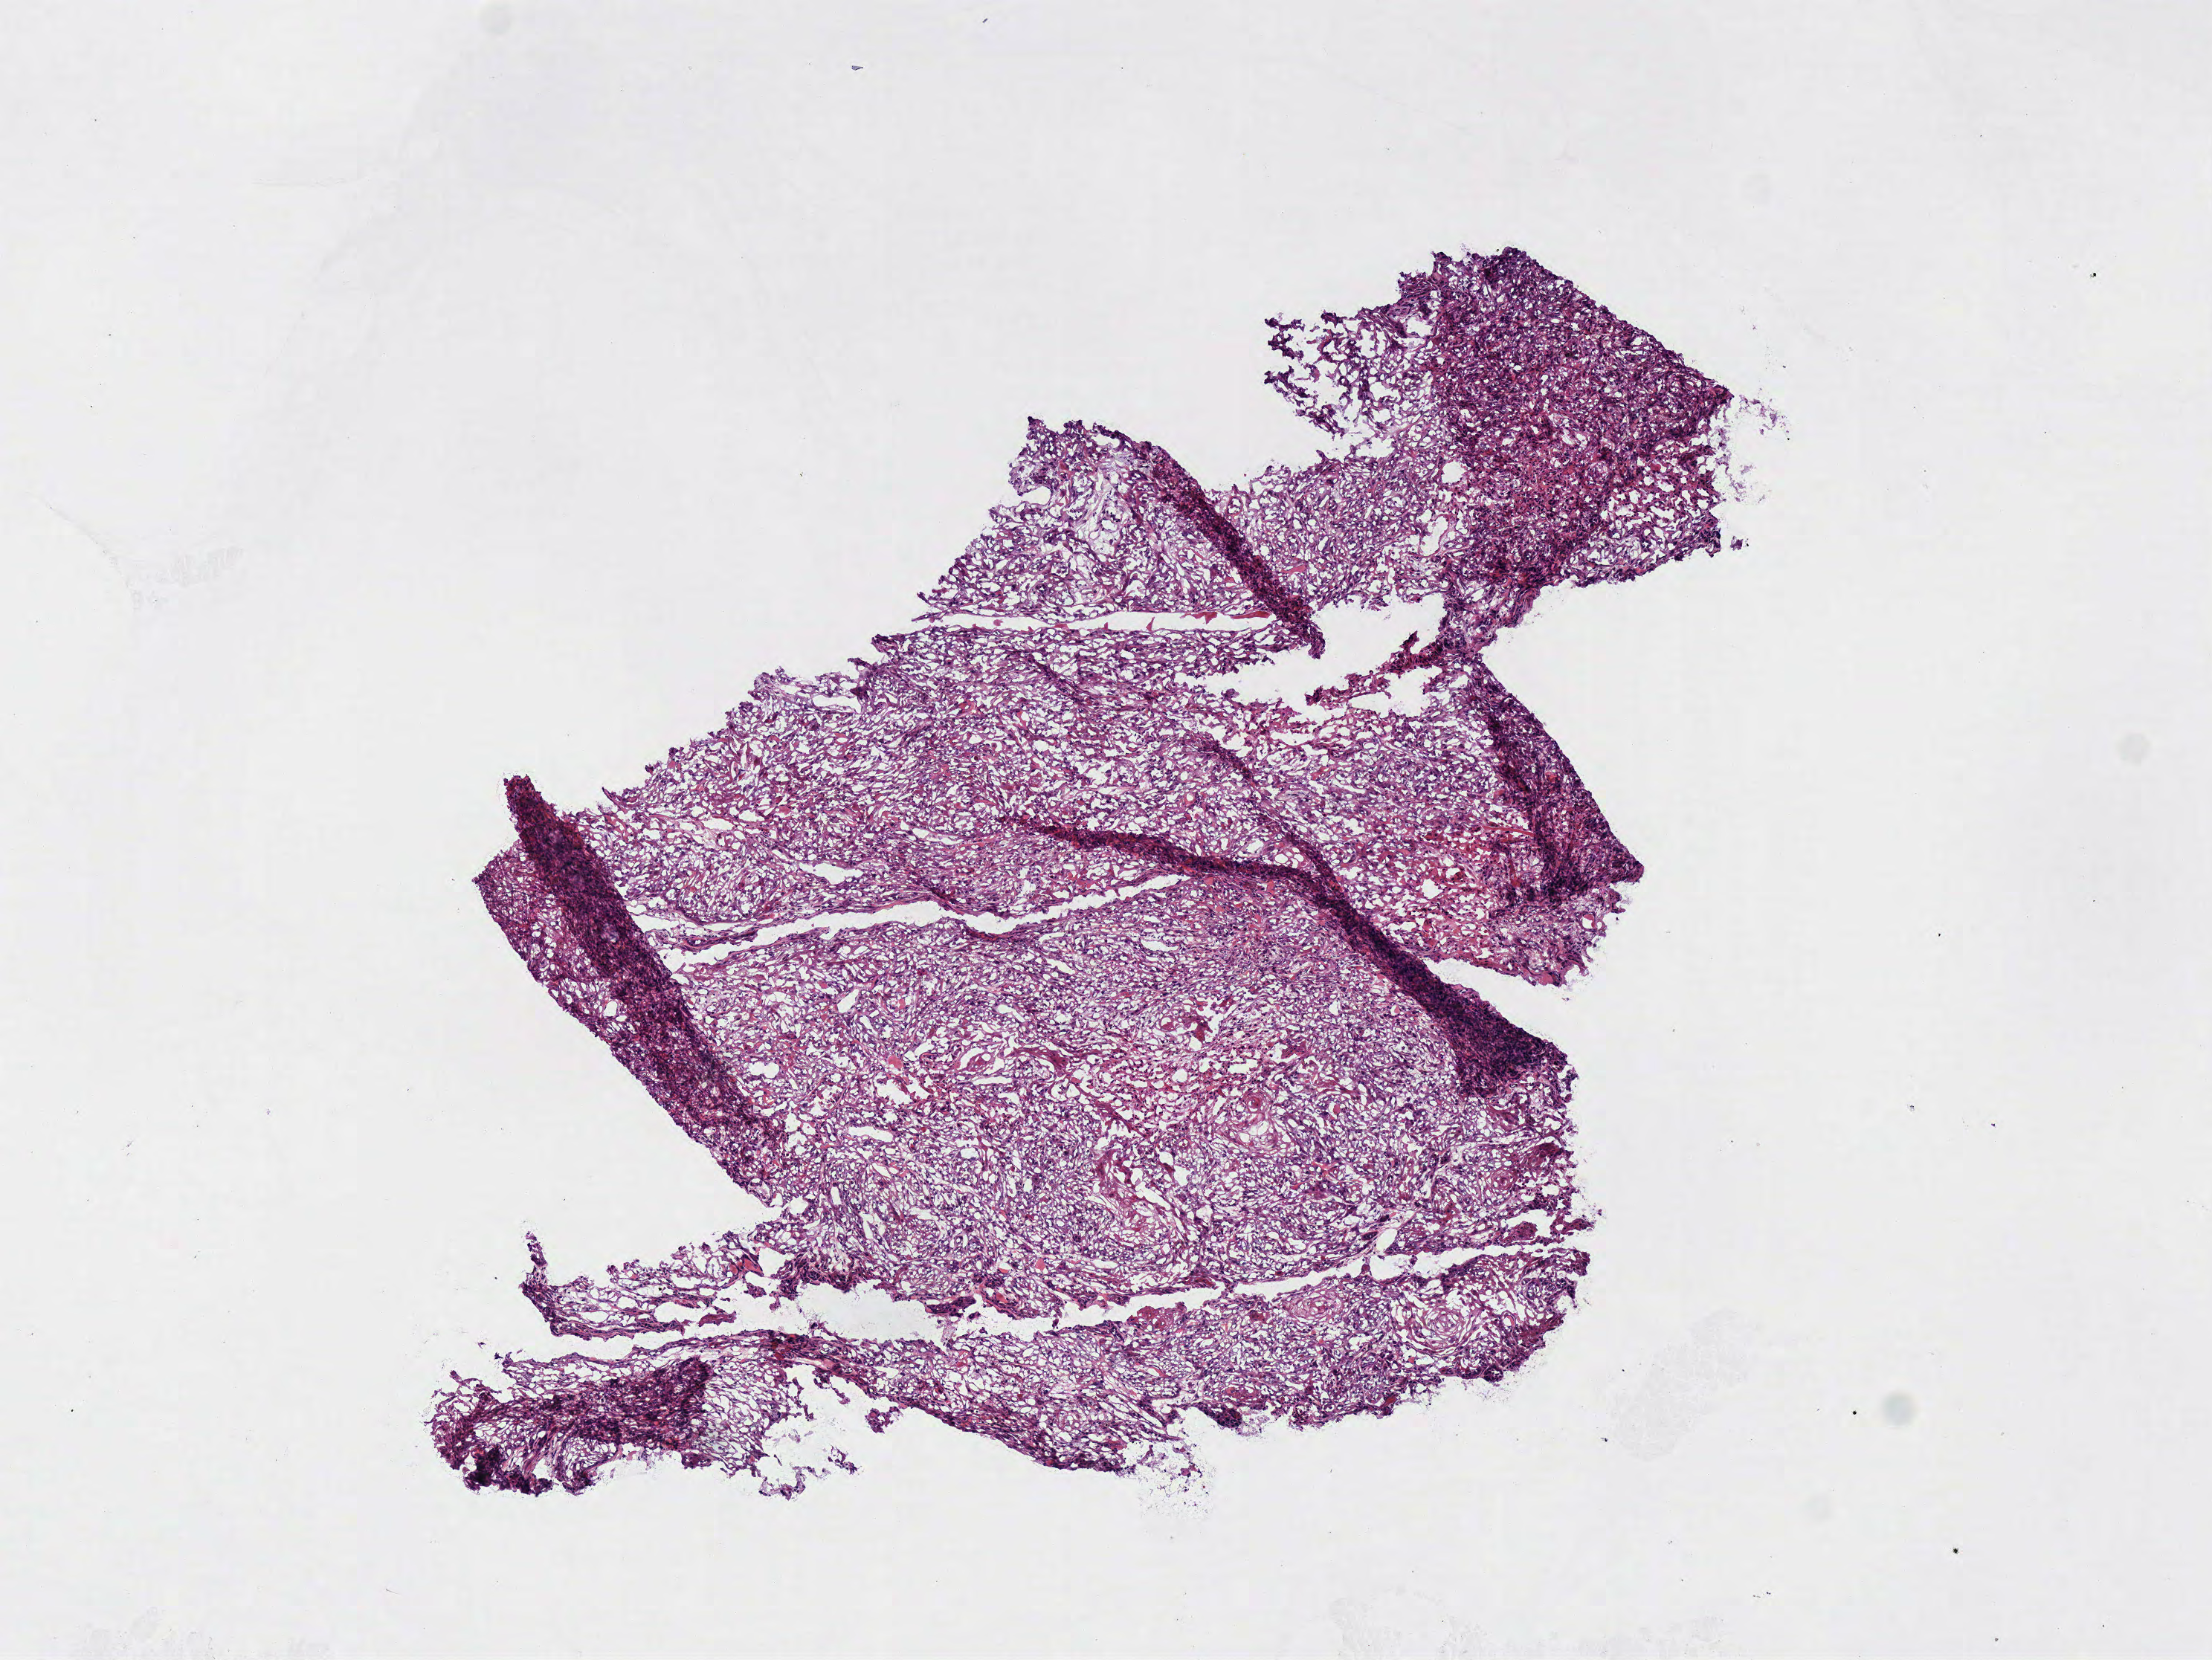
Whole-slide histology image, H&E-stained — whole scanned area (about 5.9 x 4.4 mm) shown as a low-resolution overview. Frozen section from the top of the tissue portion. Sample: primary tumour, head and neck. Patient: male, age at initial diagnosis 26 years. Histologic grade: G2 (moderately differentiated). Composition of this section per pathologist review: tumour cells 95%, tumour nuclei 85%, normal cells 0%, stromal cells 5%, necrosis 0%.
Histologic diagnosis: Squamous cell carcinoma, NOS (tongue, NOS). Lymph nodes positive (case pathology): 2 of 55 examined. TNM: T2 N2b. AJCC pathologic stage: IVA (7th edition).